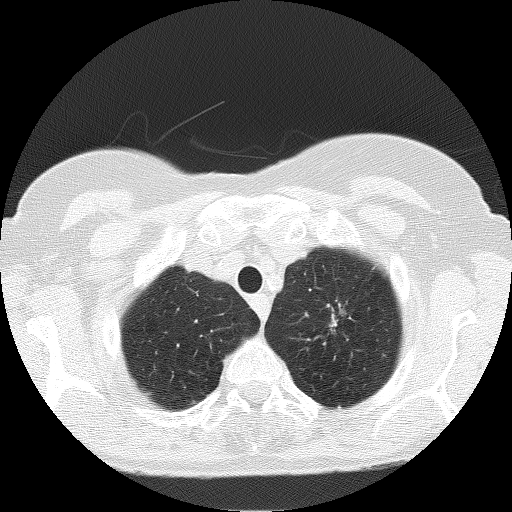
Low-dose screening chest CT, one axial slice; slice 148 of 166 in the series (ordered by position); reconstruction kernel FC51; 120 kVp; lung window (W 1500 / L -600 HU); 2 mm slice thickness; 512 × 512 image matrix, field of view 303 × 303 mm.
Annotated regions visible in this slice (expert manual segmentation):
- lesion 3 (nodule, upper lobe of left lung): bounding box [x1, y1, x2, y2] px = [332, 321, 335, 328]